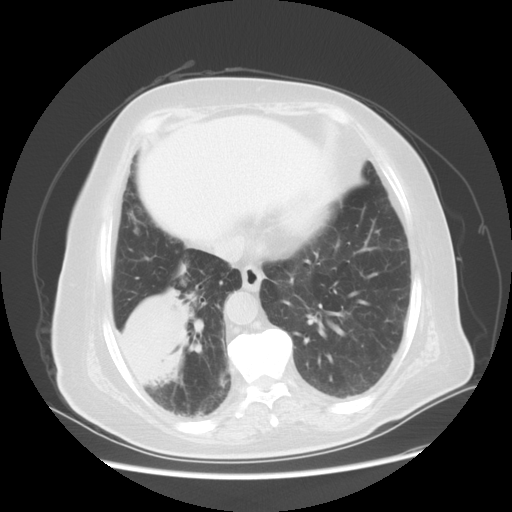
Chest CT, one axial slice; position 18 of 56 along the scan axis; reconstruction kernel STANDARD; lung window (W 1500 / L -600 HU); 5 mm slice thickness; 512 × 512 image matrix, field of view 378 × 378 mm. Patient: female, 73 years. From the clinical record (not read from this slice): clinical TNM (as recorded): T3 N0 M0.
Outlined on this slice (rectangle marked by the reading radiologist):
- lung tumour (recorded histology: adenocarcinoma): bounding box (x1, y1, x2, y2) in pixels: (114, 278, 194, 392)